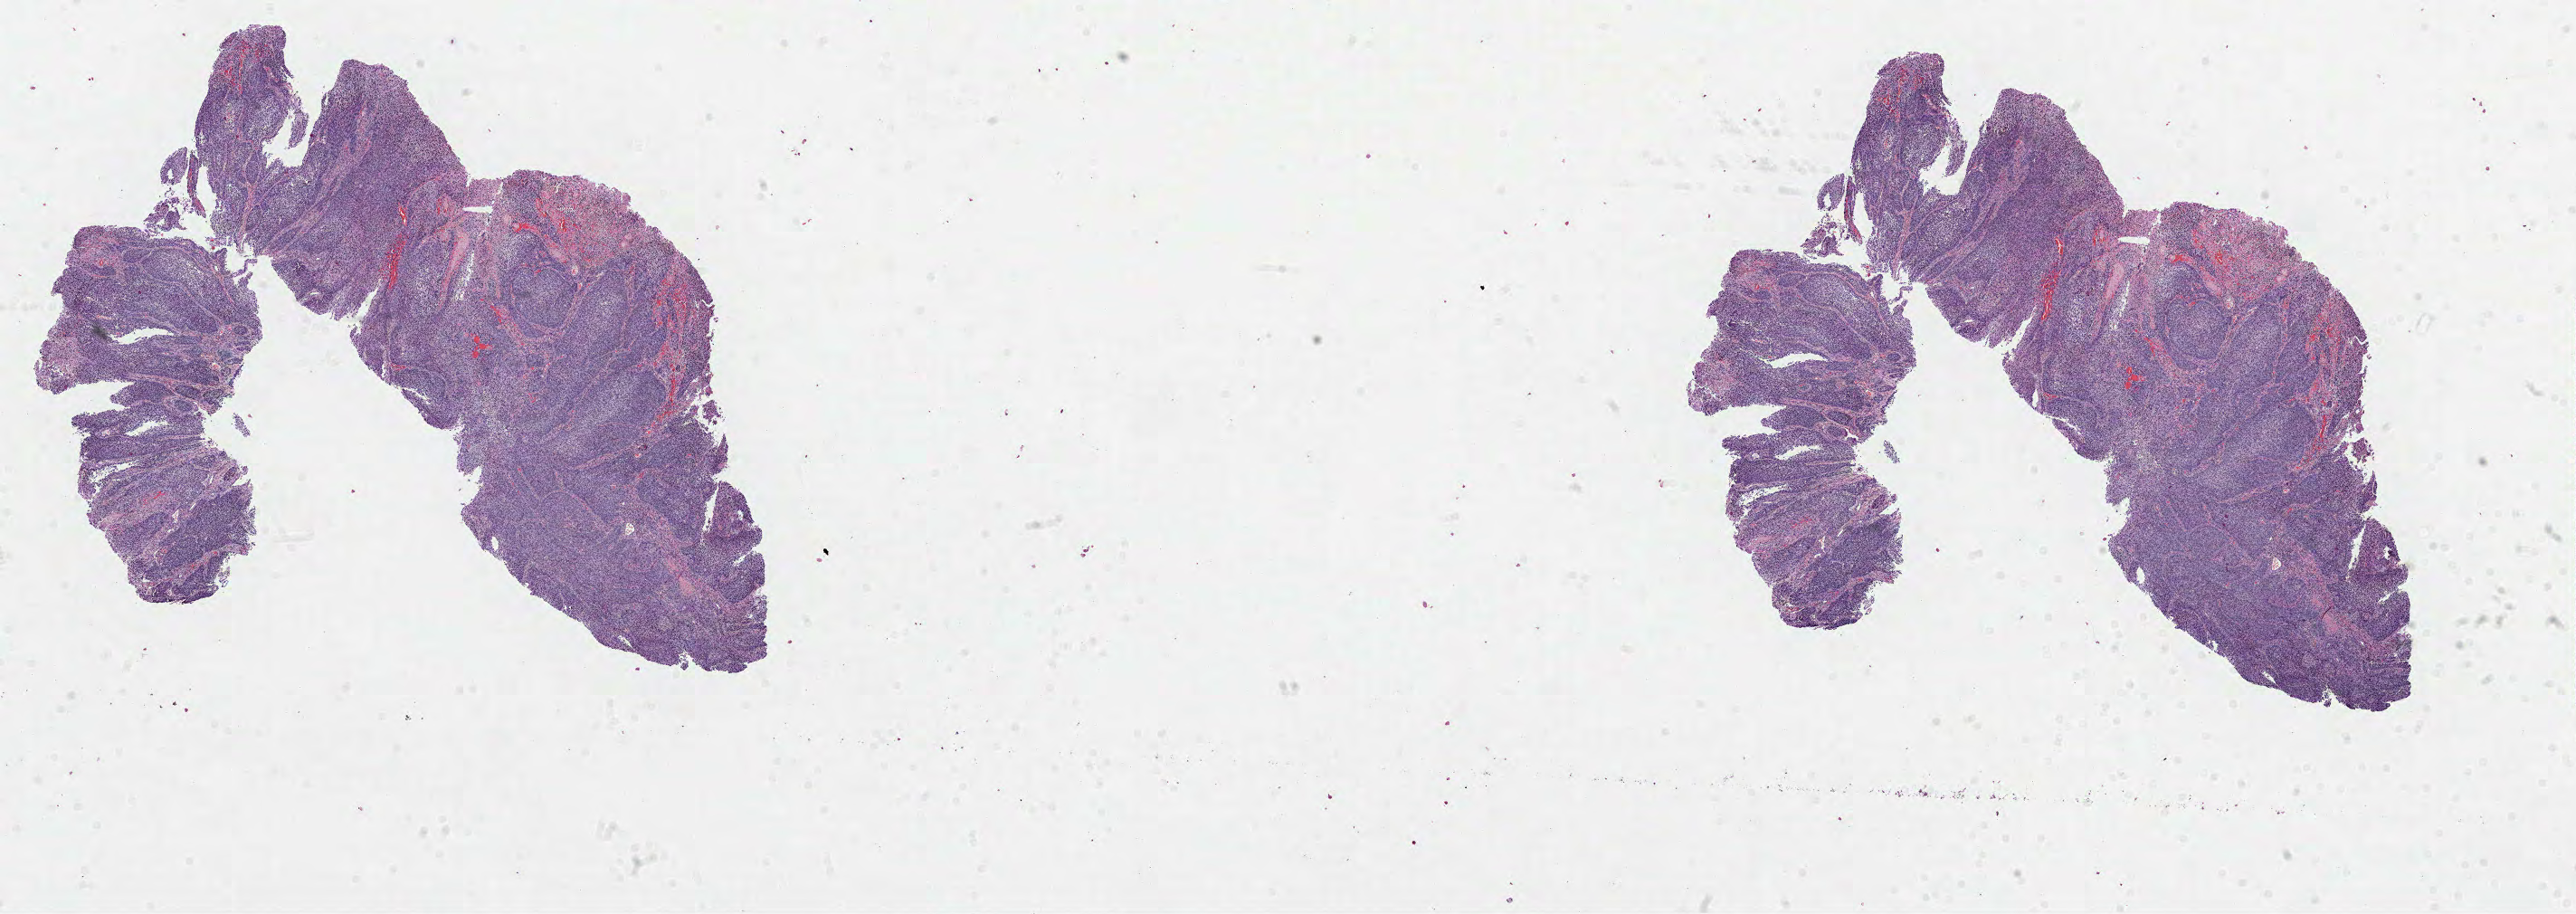
Hematoxylin and eosin (H&E) stained whole-slide image — shown as a low-resolution overview of the whole scanned area (about 23.0 x 8.1 mm). Formalin-fixed paraffin-embedded (FFPE) diagnostic section. Head and neck, primary tumour sample. Male patient; age at initial diagnosis 56 years. Histologic grade: G2 (moderately differentiated).
* diagnosis: Squamous cell carcinoma, NOS
* AJCC pathologic stage: IVA